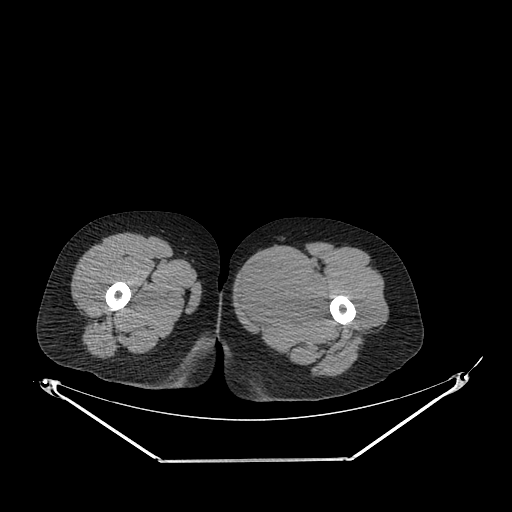
CT of an extremity soft-tissue mass (from a PET/CT study), one axial slice; slice 241 of 267 in the series (ordered by position); soft-tissue window (W 400 / L 40 HU); 3.75 mm slice thickness; 512 × 512 image matrix. Female patient. Case-level facts recorded for this patient, not image findings: histological type: pleiomorphic leiomyosarcoma; grade: intermediate; site of the primary tumour: left thigh.
Annotated regions visible in this slice (expert contour drawn on MRI and transferred to this co-registered scan by the dataset authors):
- gross tumour volume including surrounding oedema: bounding box <237,258,328,330> (left, top, right, bottom; pixels)
- gross tumour volume (mass): <237,260,327,330>